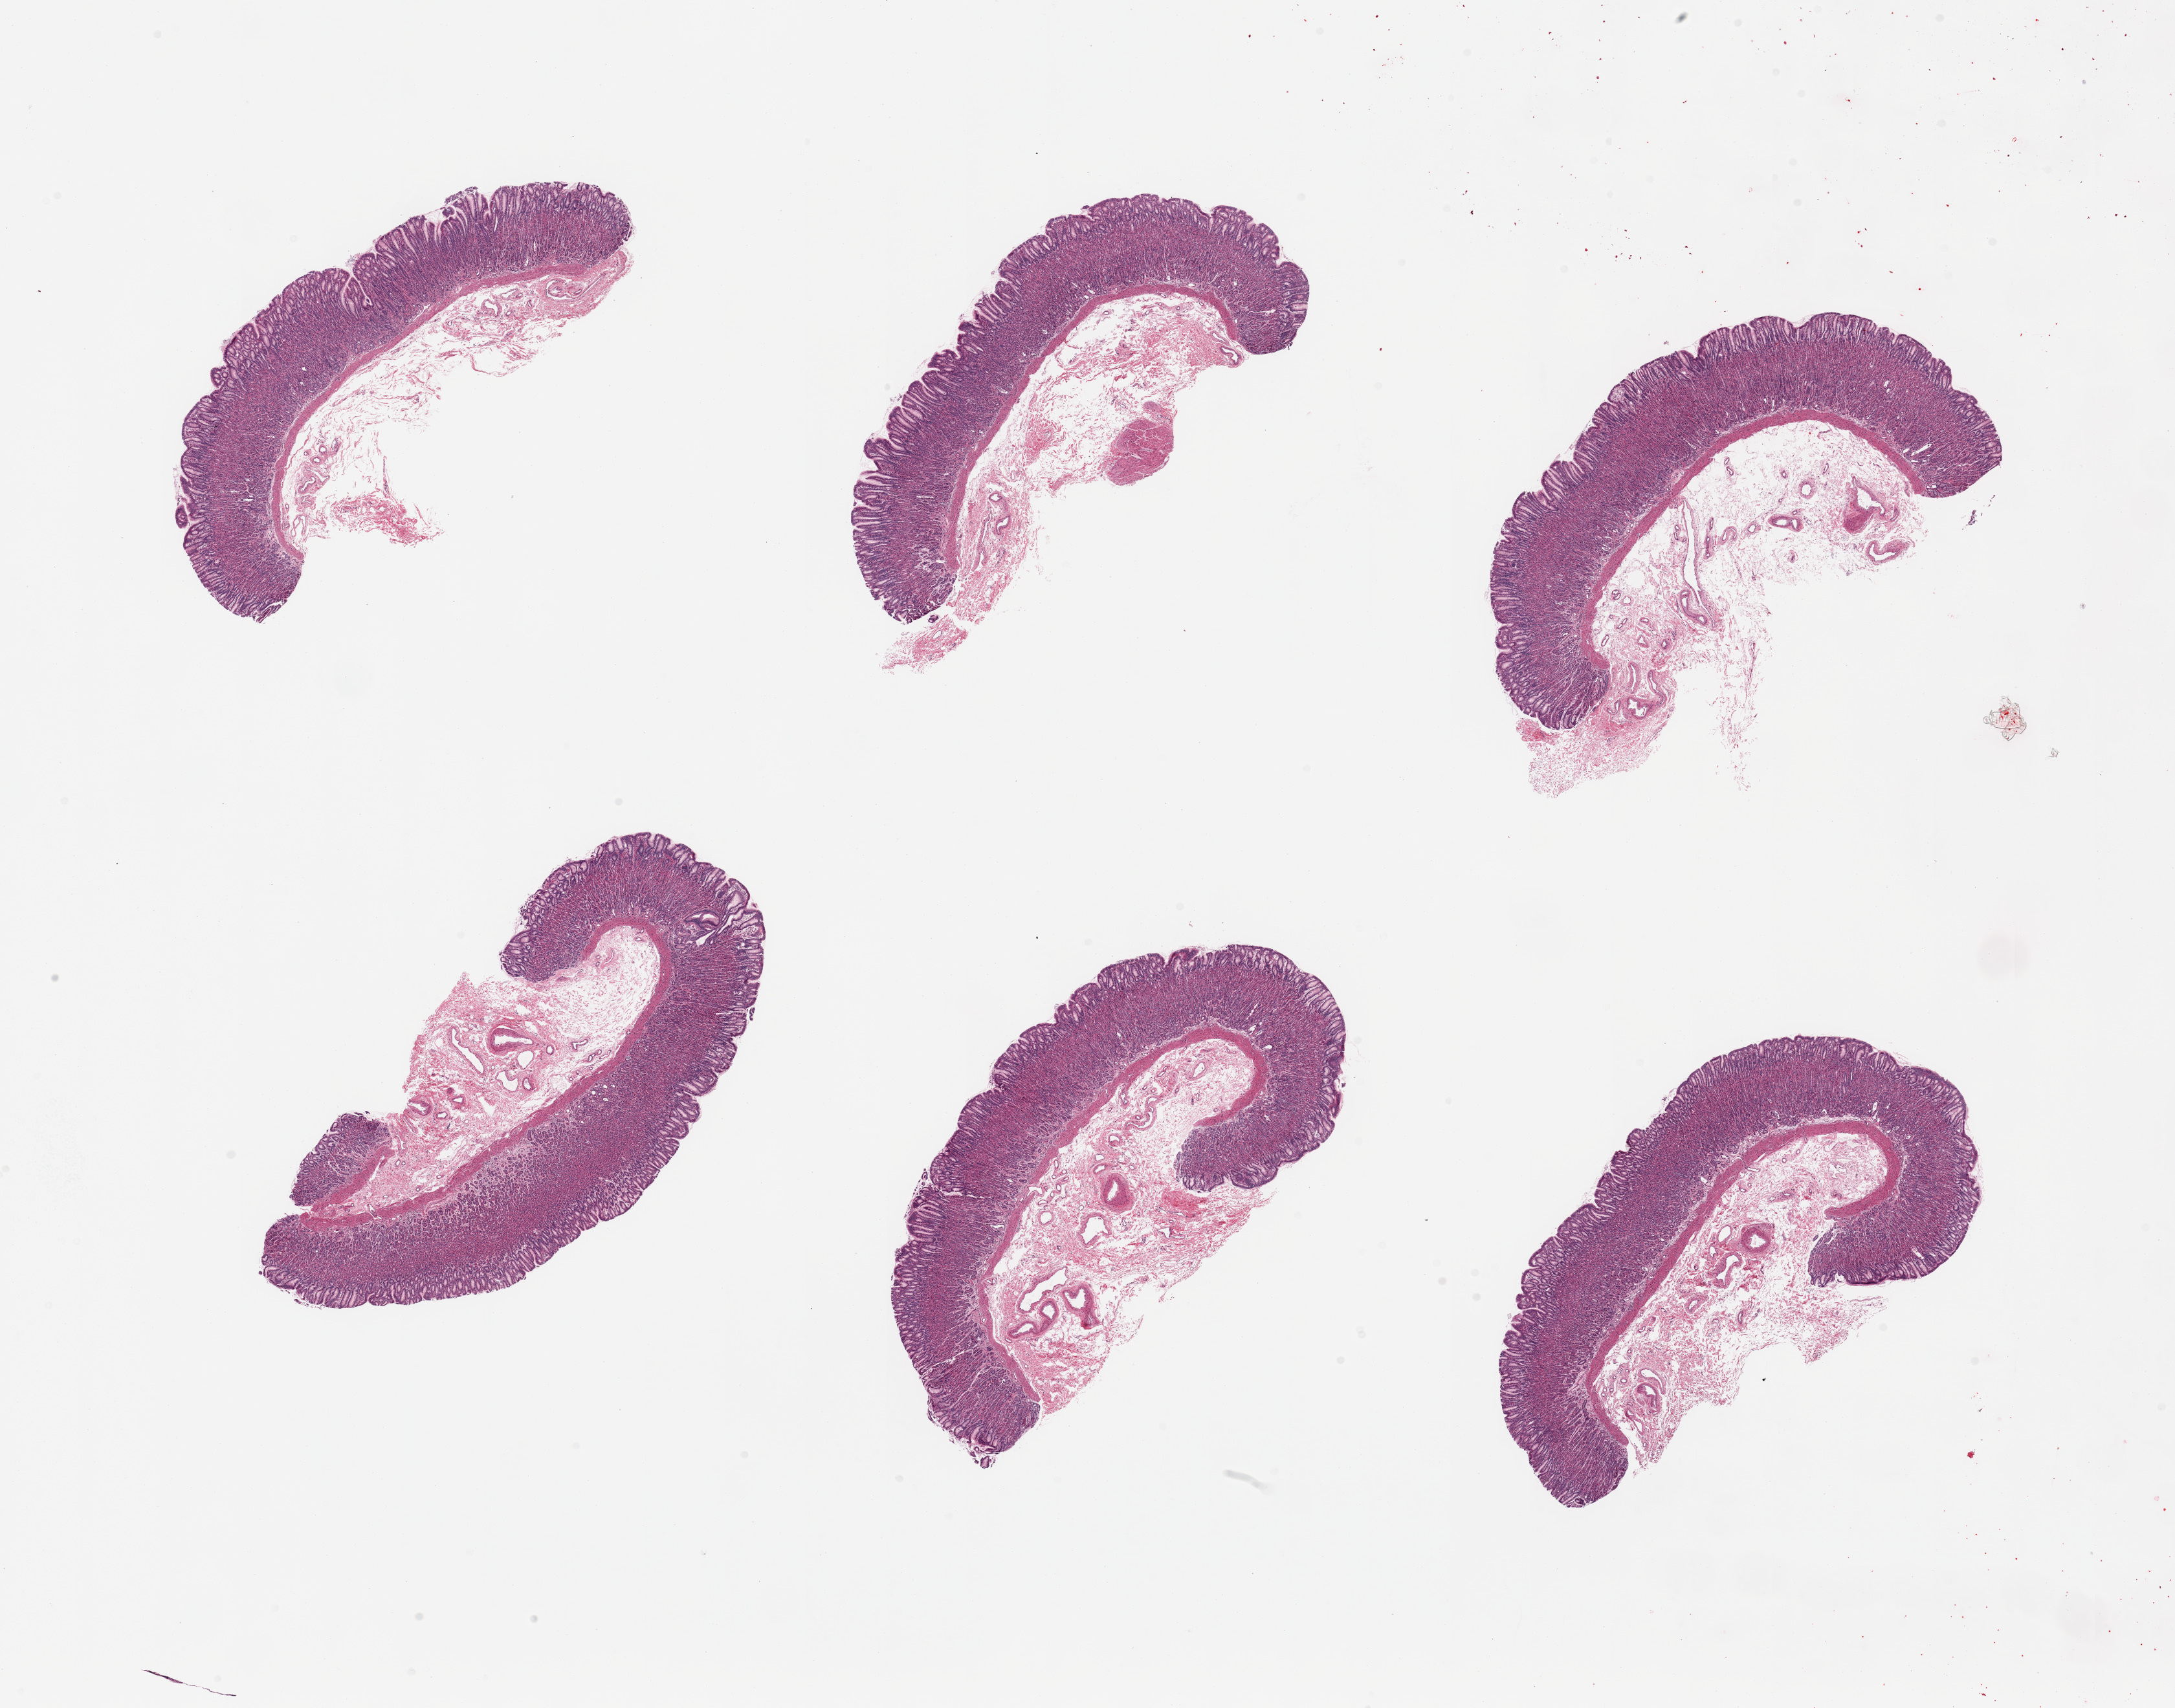
H&E whole-slide image, low-resolution overview of the scanned area, about 26.6 x 20.9 mm (slide scanned at 20x), PAXgene-fixed paraffin-embedded (PFPE) section, target tissue: stomach, donor tissue sample. Donor sex: male.
Pathologist's review note for this sample: 6 pieces; well preserved, well dissected mucosa, no muscularis propria; focal basal gland dilatation, degeneration.